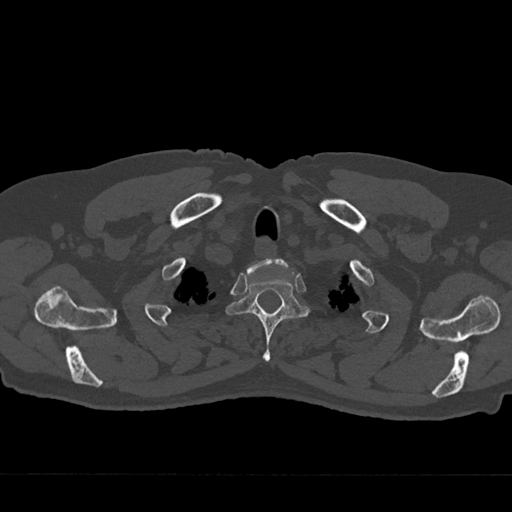
CT including the spine, one axial slice; slice 620 of 797 in the series (ordered by position); 120 kVp; bone window (W 1800 / L 400 HU); 0.5 mm slice thickness; 512 × 512 image matrix, field of view 377 × 377 mm. Patient: male, 75 years. From the clinical record (not read from this slice): primary cancer: renal; vertebrae with lytic lesions (as recorded): T4.
Structures marked on this image (semi-automatic segmentation, software-assisted and operator-edited):
- T1 vertebra: bounding box <246,258,290,276> (left, top, right, bottom; pixels)
- T2 vertebra: <225,276,310,362>